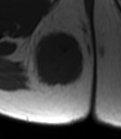
MRI of an extremity soft-tissue mass, one axial slice. Position 22 of 47 along the scan axis. MR volume resampled by the dataset authors to the PET/CT grid (not the native acquisition matrix). 3.27 mm slice thickness. 121 × 139 image matrix. Female patient. Case-level facts recorded for this patient, not image findings: histological type: epithelioid sarcoma; grade: intermediate; site of the primary tumour: right buttock.
Annotated regions visible in this slice (expert contour drawn on MRI and transferred to this co-registered scan by the dataset authors):
- gross tumour volume including surrounding oedema: bounding box <29,29,83,90> (left, top, right, bottom; pixels)
- gross tumour volume (mass): <32,34,83,87>